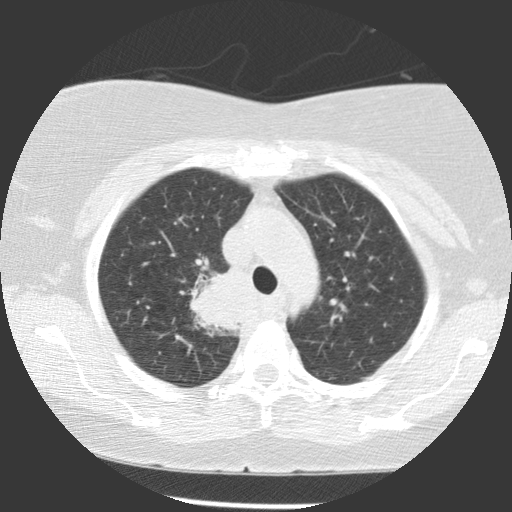
Chest CT (low-dose screening protocol), one axial image. First (baseline) screen. Lung window (W 1500 / L -600 HU). Standard (soft-tissue) reconstruction kernel (STANDARD). 140 kVp. 512 × 512 image matrix. Female participant, aged 63 years at enrolment.
Expert reader's lesion annotation, bounding box <196,265,255,326> (left, top, right, bottom; pixels). Reader record for this screening exam (exam-level; its link to the box is not recorded): non-calcified nodule or mass ≥4 mm, right upper lobe, 39 × 36 mm, spiculated (stellate) margins, soft tissue attenuation.